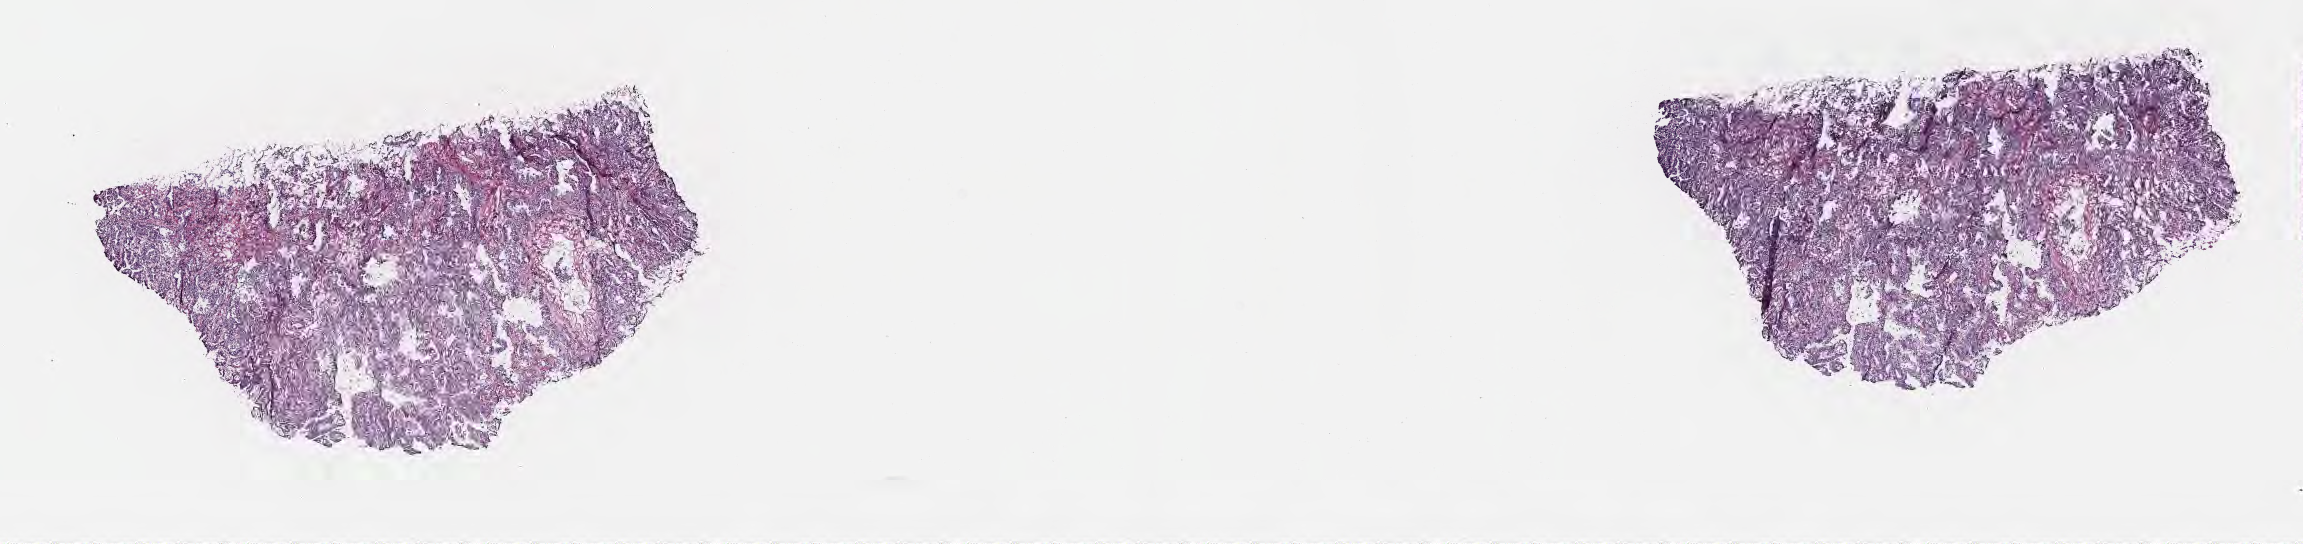
Digitized haematoxylin and eosin-stained section, shown as a low-resolution overview of the whole scanned area (about 18.6 x 4.4 mm). Cryosection. Primary tumor. Site: upper lobe of left lung. Patient male; aged 62. Pathologist review of this section (percent, as recorded): tumor cells 72%, tumor nuclei 90%, stromal cells 23%, necrosis 3%, normal cells 2%. Inflammatory infiltration, as recorded: lymphocyte infiltration 4%, monocyte infiltration 1%, neutrophil infiltration 0%.
* AJCC pathologic stage: Stage IA
* diagnosis: Adenocarcinoma with mixed subtypes
* section: top of the tissue portion